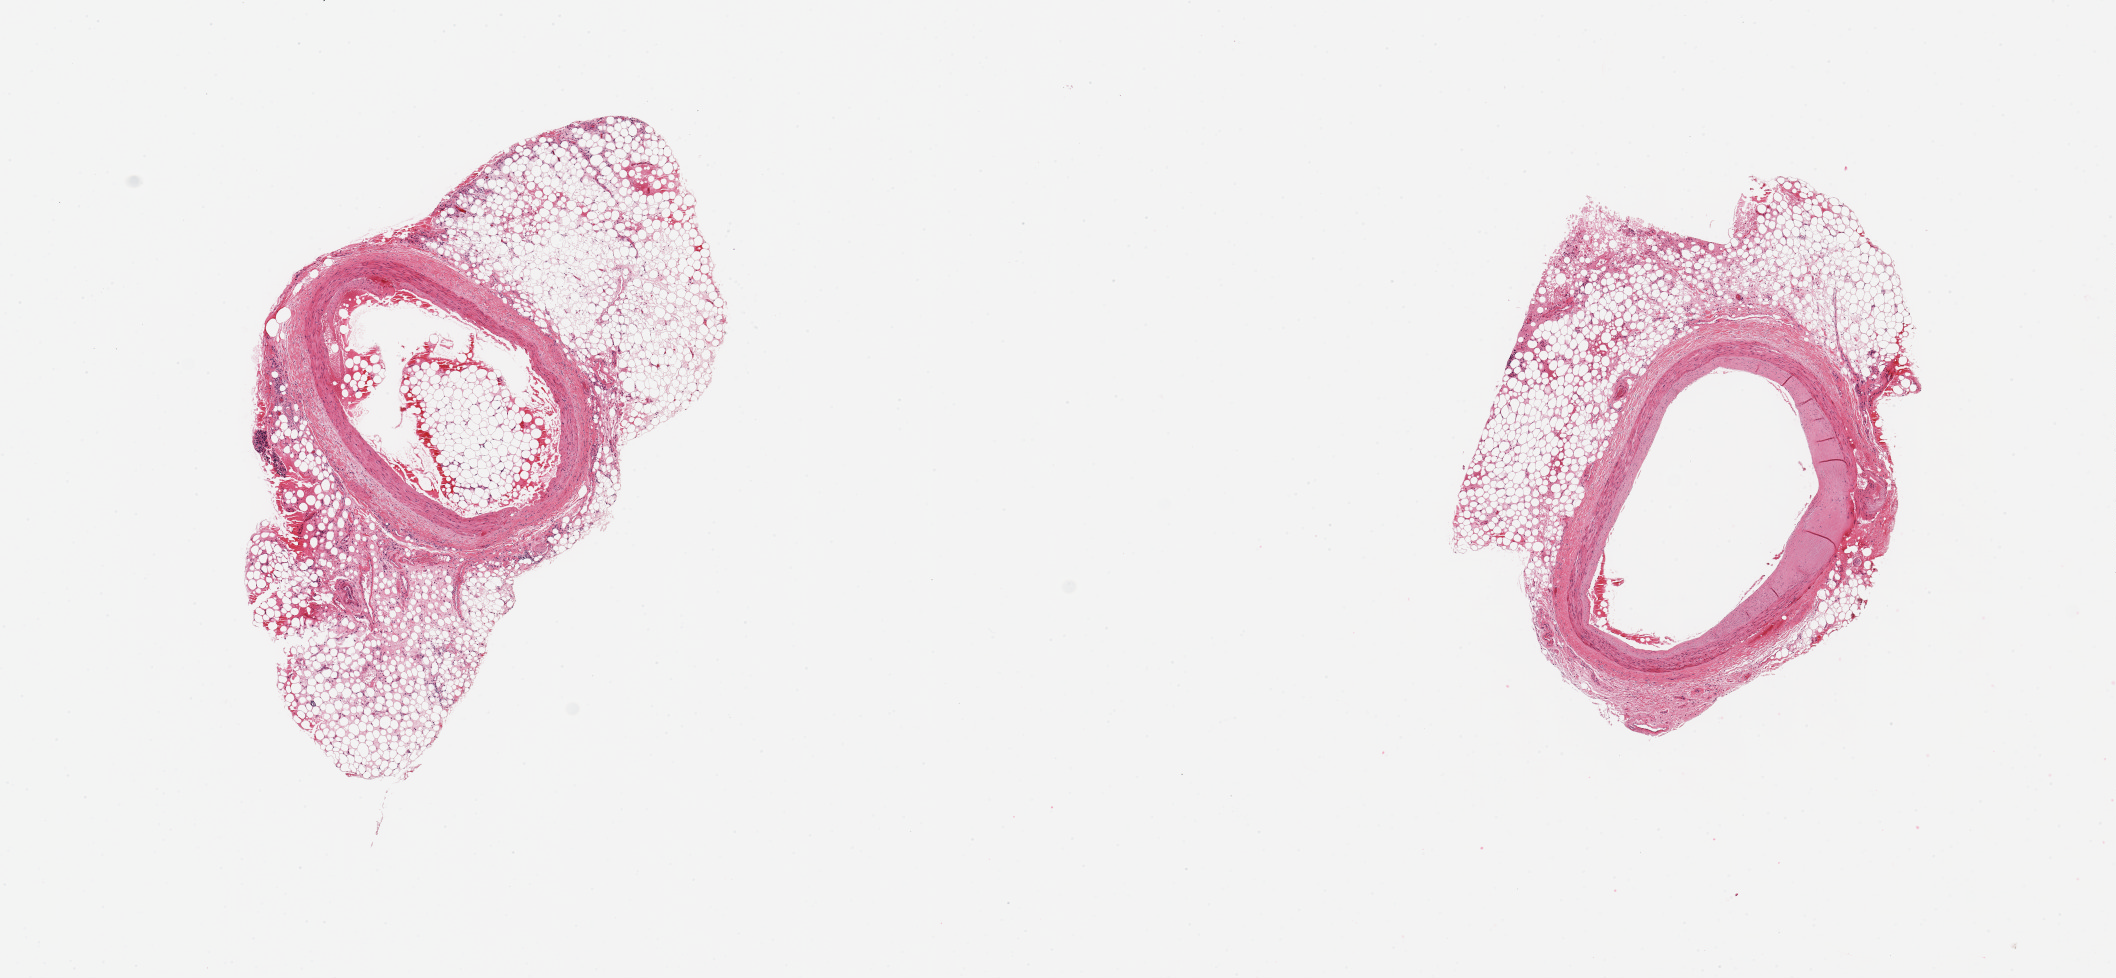
Whole-slide image, H&E stain, shown as a low-resolution overview of the whole scanned area (about 16.7 x 7.7 mm, from a 20x scan), PAXgene-fixed paraffin-embedded (PFPE) section, sampled site (target tissue): coronary artery, tissue donor sample. Donor: male.
Reviewer comment on this tissue sample: 2 pieces, rims of adherent fat, 1-2mm, minimal occlusive atherosis.